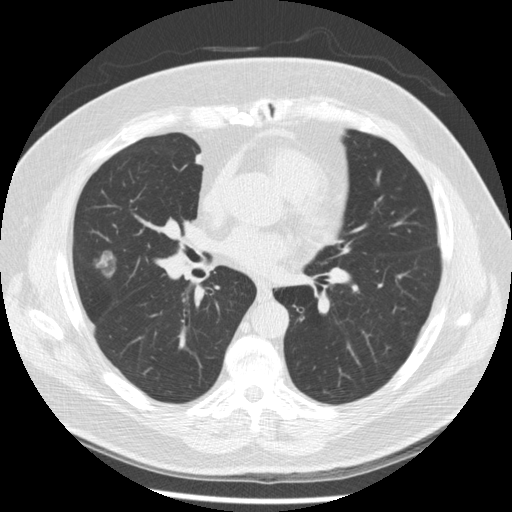
Low-dose screening chest CT, axial slice, second annual screen, lung window (W 1500 / L -600 HU), 120 kVp, 512 × 512 image matrix. Male, age 67 years at enrolment.
Lesion marked by an expert reader, bounding box <82,245,123,287> (left, top, right, bottom; pixels). The exam's reader record, not a measurement of the box and not confirmed to be the same lesion: non-calcified nodule or mass ≥4 mm, right middle lobe, 19 × 16 mm, smooth margins, soft tissue attenuation, pre-existing on the prior screen: yes; interval growth: yes. Official screen result: positive, other. Lung cancer was diagnosed 47 days after this screen: adenocarcinoma, NOS, right middle lobe, moderately differentiated (G2), stage IA (AJCC 6th edition), 14 mm at pathology.